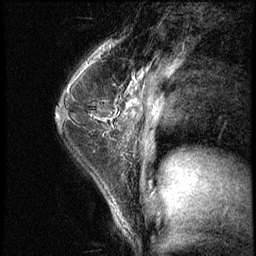
Breast MRI (dynamic contrast-enhanced), one sagittal slice. Slice 42 of 62 in the series (ordered by position). 3 images stored at this slice position (order not interpretable as contrast timing). 1.5 T. TE 4.2 ms, TR 8.7 ms. 2.5 mm slice thickness. 256 × 256 image matrix. Female patient, age 35 years. From the clinical record (not read from this slice): setting: breast cancer imaged before/during neoadjuvant chemotherapy; receptor status: HER2-positive.
Outlined on this slice (semi-automatically segmented with operator editing):
- analysis volume of interest (the breast-tissue region the enhancement analysis was run in; not a lesion): bounding box [x1, y1, x2, y2] px = [71, 78, 120, 139]
- tumour enhancement mask (voxels above the 140 % enhancement threshold inside the analysis volume of interest): [93, 115, 113, 120]